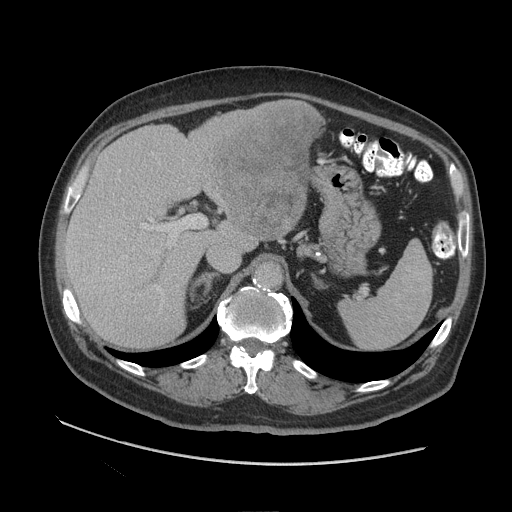
Contrast-enhanced abdominal CT (liver protocol), one axial slice. Slice 60 of 109 in the series (ordered by position). Reconstruction kernel STANDARD. 140 kVp. Soft-tissue window (W 400 / L 40 HU). 2.5 mm slice thickness. 512 × 512 image matrix, field of view 420 × 420 mm. From the clinical record (not read from this slice): diagnosis: hepatocellular carcinoma (patient treated with transarterial chemoembolisation; whether this scan precedes or follows treatment is not stated here); TNM stage (as recorded): Stage-I; Child-Pugh class: A; tumour nodularity: uninodular.
Structures marked on this image (semi-automatically segmented with operator editing):
- liver parenchyma outside the tumour (the mass and vessels are separate outlines, so this box may not span the whole liver): box from (x=64, y=110) to (x=287, y=348) px
- mass: (x=189, y=99)–(x=325, y=239)
- liver vessels: (x=84, y=218)–(x=184, y=302)